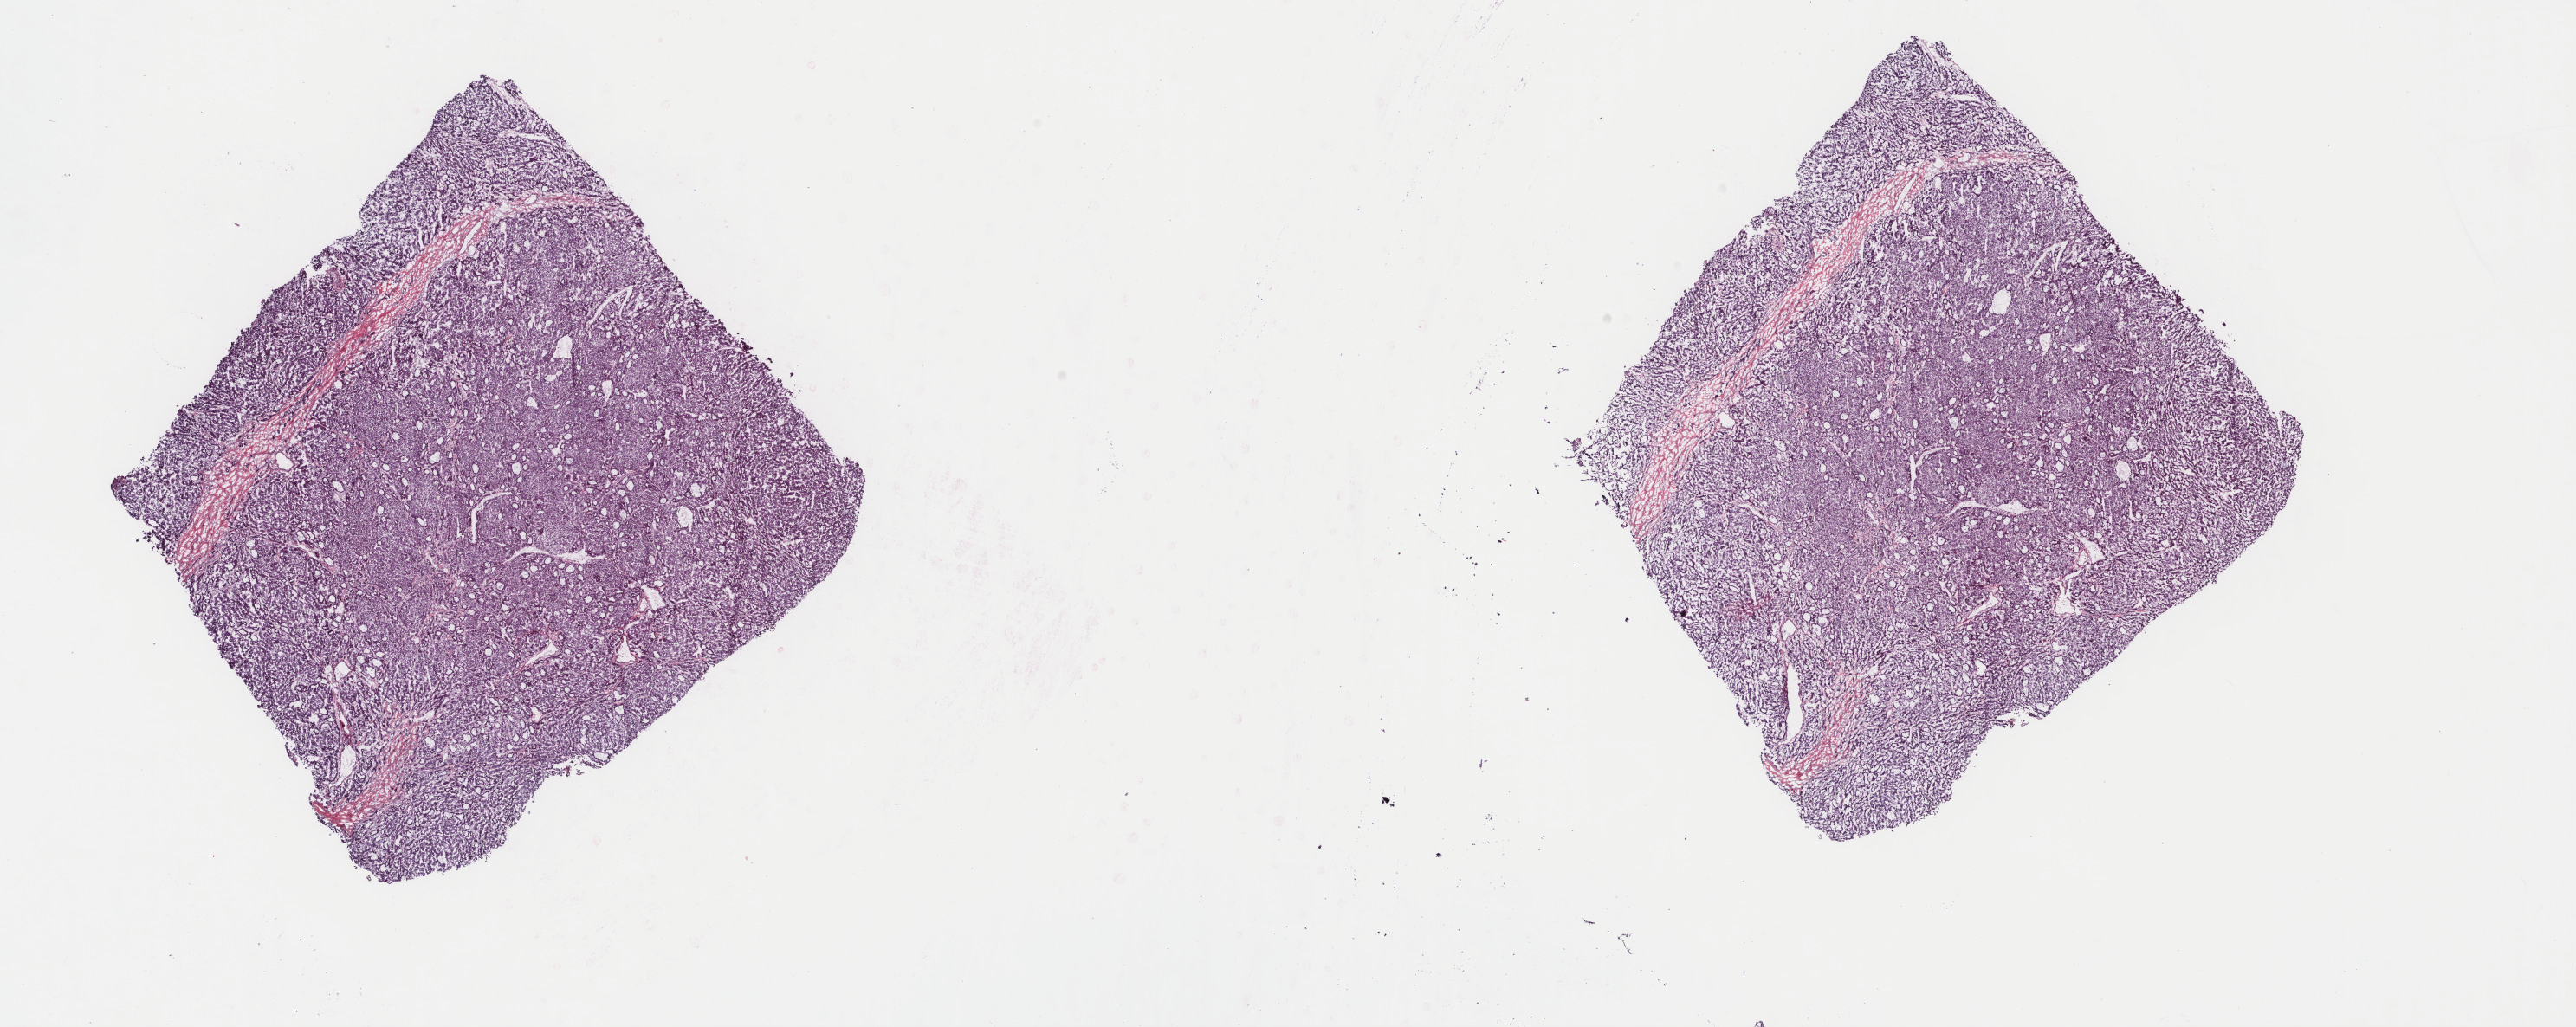
H&E whole-slide image — shown as a low-resolution overview of the whole scanned area (about 23.6 x 9.4 mm, slide scanned at 40x); frozen section; sample: primary tumour, liver. Female patient; age at initial diagnosis 80 years. Histologic grade: G2 (moderately differentiated). Composition of this section per pathologist review: tumour cells 90%, tumour nuclei 100%, normal cells 0%, stromal cells 10%, necrosis 0%. Infiltration values recorded for this section: lymphocyte infiltration 4%, monocyte infiltration 3%, neutrophil infiltration 0%.
- AJCC pathologic stage: IIIA
- histologic diagnosis: Hepatocellular carcinoma, NOS
- TNM: T3 N0 M0